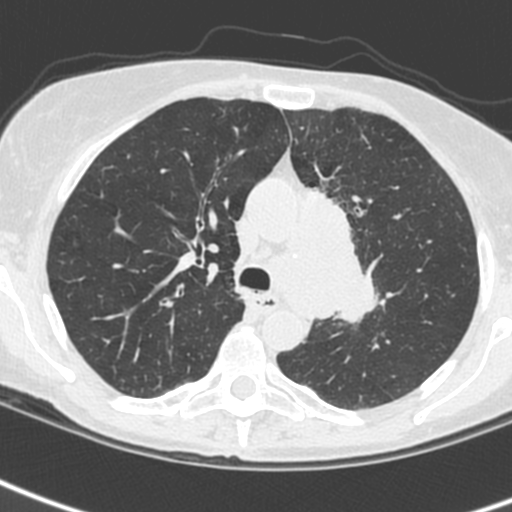
Low-dose screening chest CT, one axial slice; slice 168 of 242 in the series (ordered by position); 120 kVp; lung window (W 1500 / L -600 HU); 1.3 mm slice thickness; 512 × 512 image matrix.
Outlined on this slice (expert manual segmentation):
- lesion 3 (tumor, upper lobe of left lung): bounding box <304,188,380,325> (left, top, right, bottom; pixels)